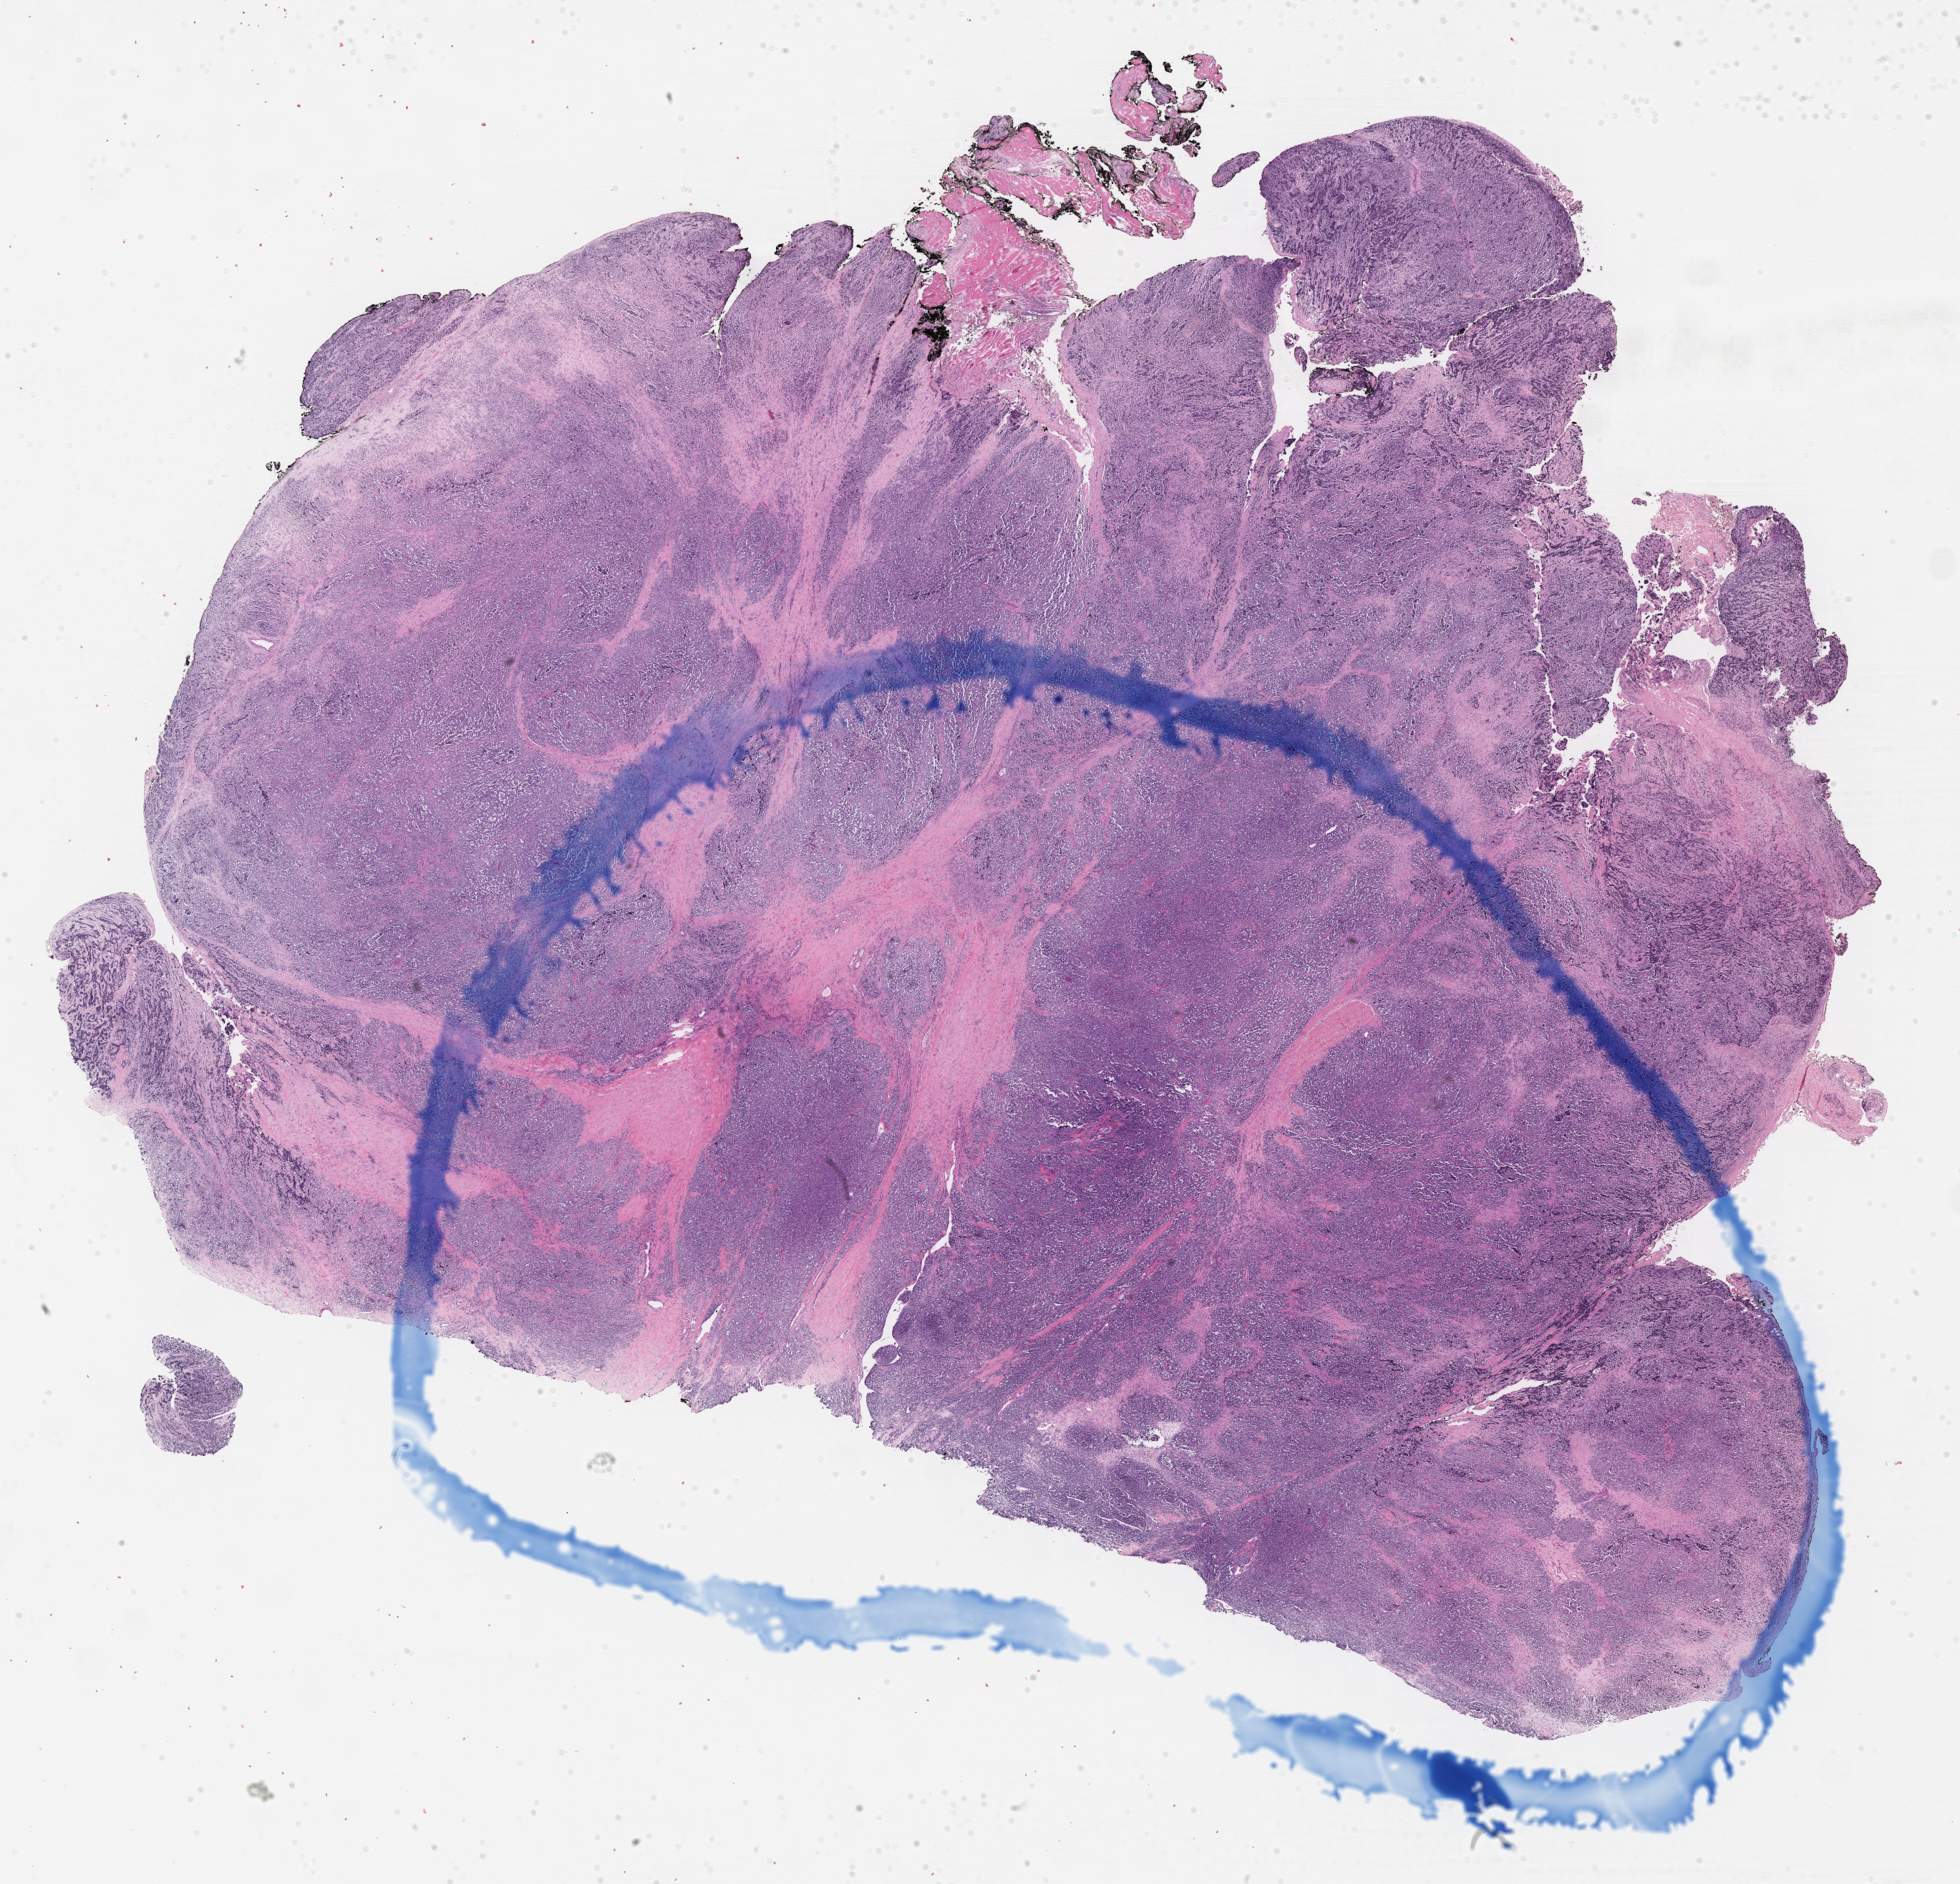
Whole-slide image, H&E stain of tumor tissue — low-resolution overview of the scanned area, about 22.1 x 21.3 mm; FFPE section; sample anatomic site: soft tissue, wrist-right. Male patient, age at diagnosis 11.3 years.
- primary site (case record): hand
- diagnosis: rhabdomyosarcoma; histological classification: alveolar rhabdomyosarcoma
- stage (as recorded): 4
- metastatic status at presentation (as recorded): metastatic (confirmed)